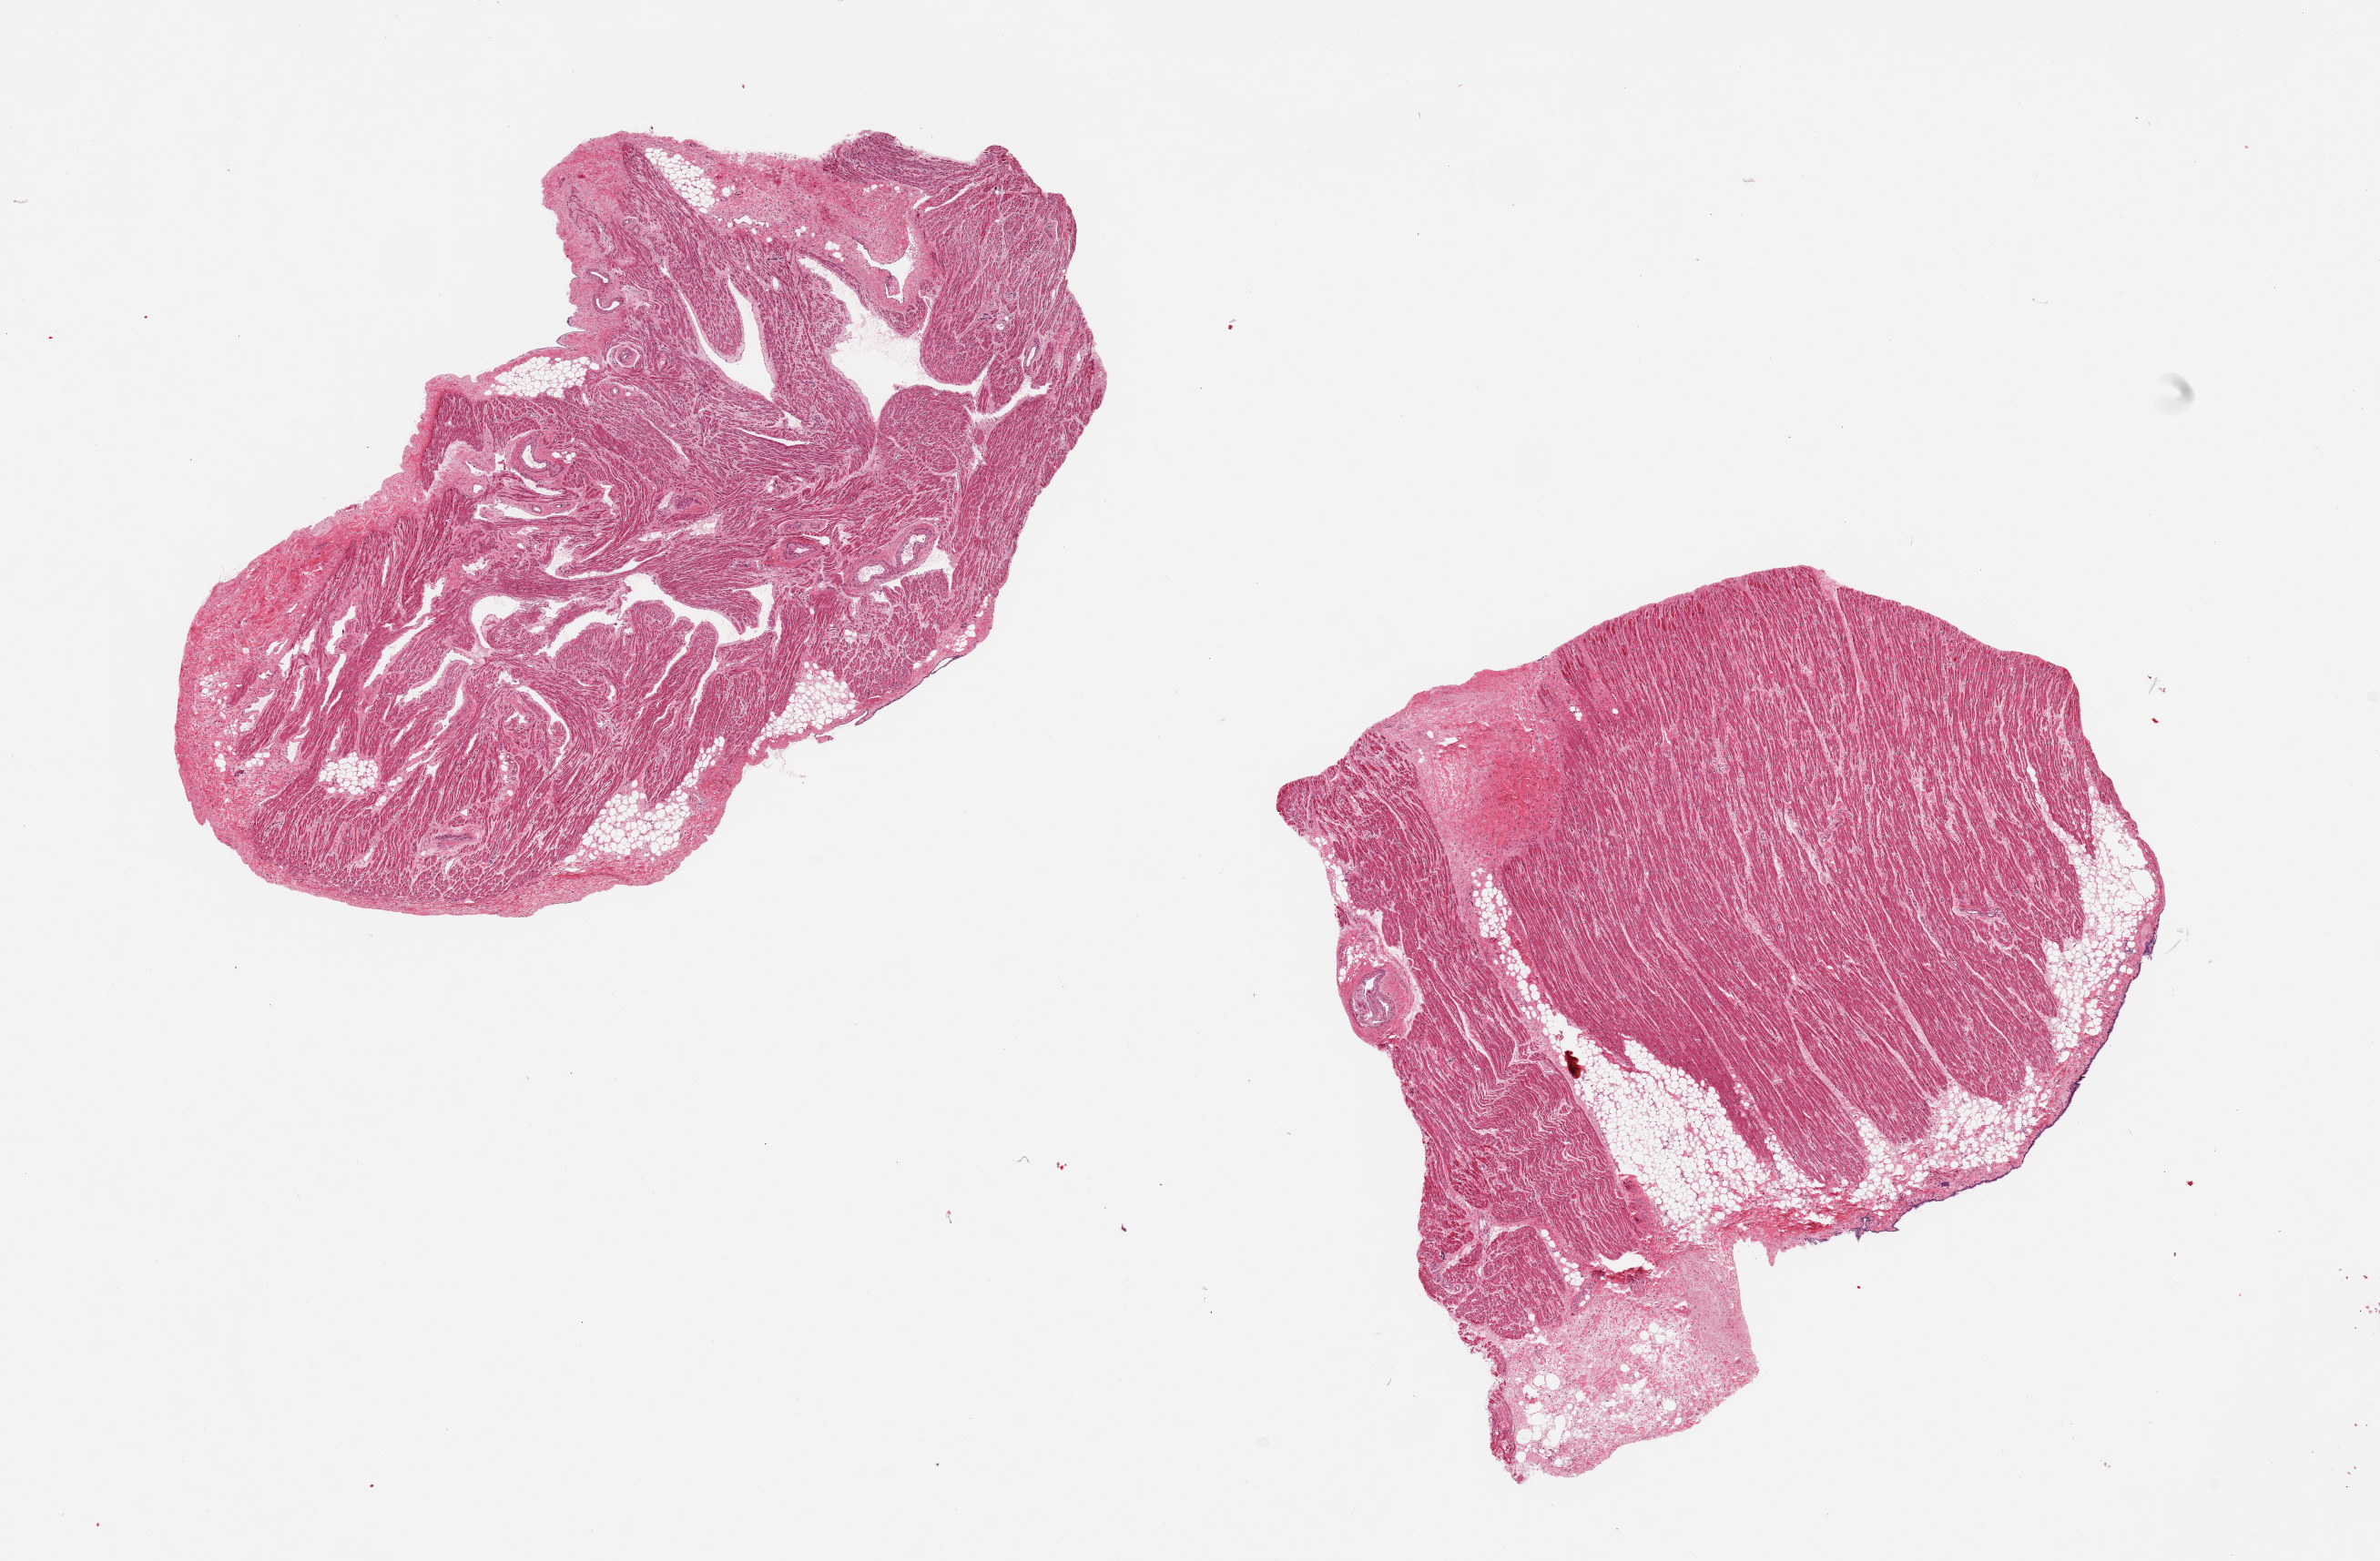
Hematoxylin and eosin (H&E) whole-slide image, shown as a low-resolution overview of the whole scanned area (about 20.7 x 13.6 mm, acquisition: 20x scan), PAXgene-fixed paraffin-embedded (PFPE) section, sampled site (target tissue): auricular appendage, tissue donor sample. Donor: male.
* pathologist's review note for this sample: 2 pieces; 1 with 20% epicardial fat. Other with <10% fat